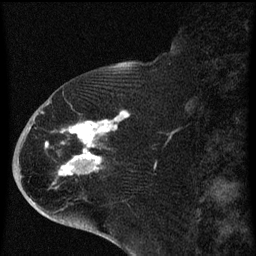
Breast MRI (dynamic contrast-enhanced), one sagittal slice. Slice 25 of 60 in the series (ordered by position). Dynamic contrast-enhanced series, image 2 of 4 at this slice position (ordered by acquisition). 1.5 T. TE 4.2 ms, TR 8 ms. 2 mm slice thickness. 256 × 256 image matrix. Female patient, age 71 years.
Annotated regions visible in this slice (semi-automatic segmentation, software-assisted and operator-edited):
- analysis volume of interest (the breast-tissue region the enhancement analysis was run in; not a lesion): bounding box [x1, y1, x2, y2] px = [32, 86, 140, 205]
- tumour enhancement mask (voxels above the 70 % enhancement threshold inside the analysis volume of interest): [42, 110, 130, 185]